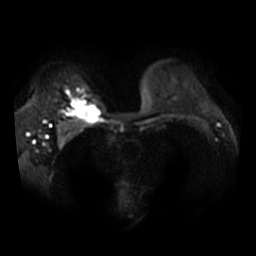
Breast MRI, one axial slice; diffusion-weighted series; image 2 of 4 stored at this slice position (different b-values; order by instance number); 3 T; 256 × 256 image matrix, field of view 340 × 340 mm. Female patient.
Outlined on this slice (expert manual segmentation):
- tumour on diffusion-weighted imaging: box from (x=71, y=101) to (x=98, y=122) px